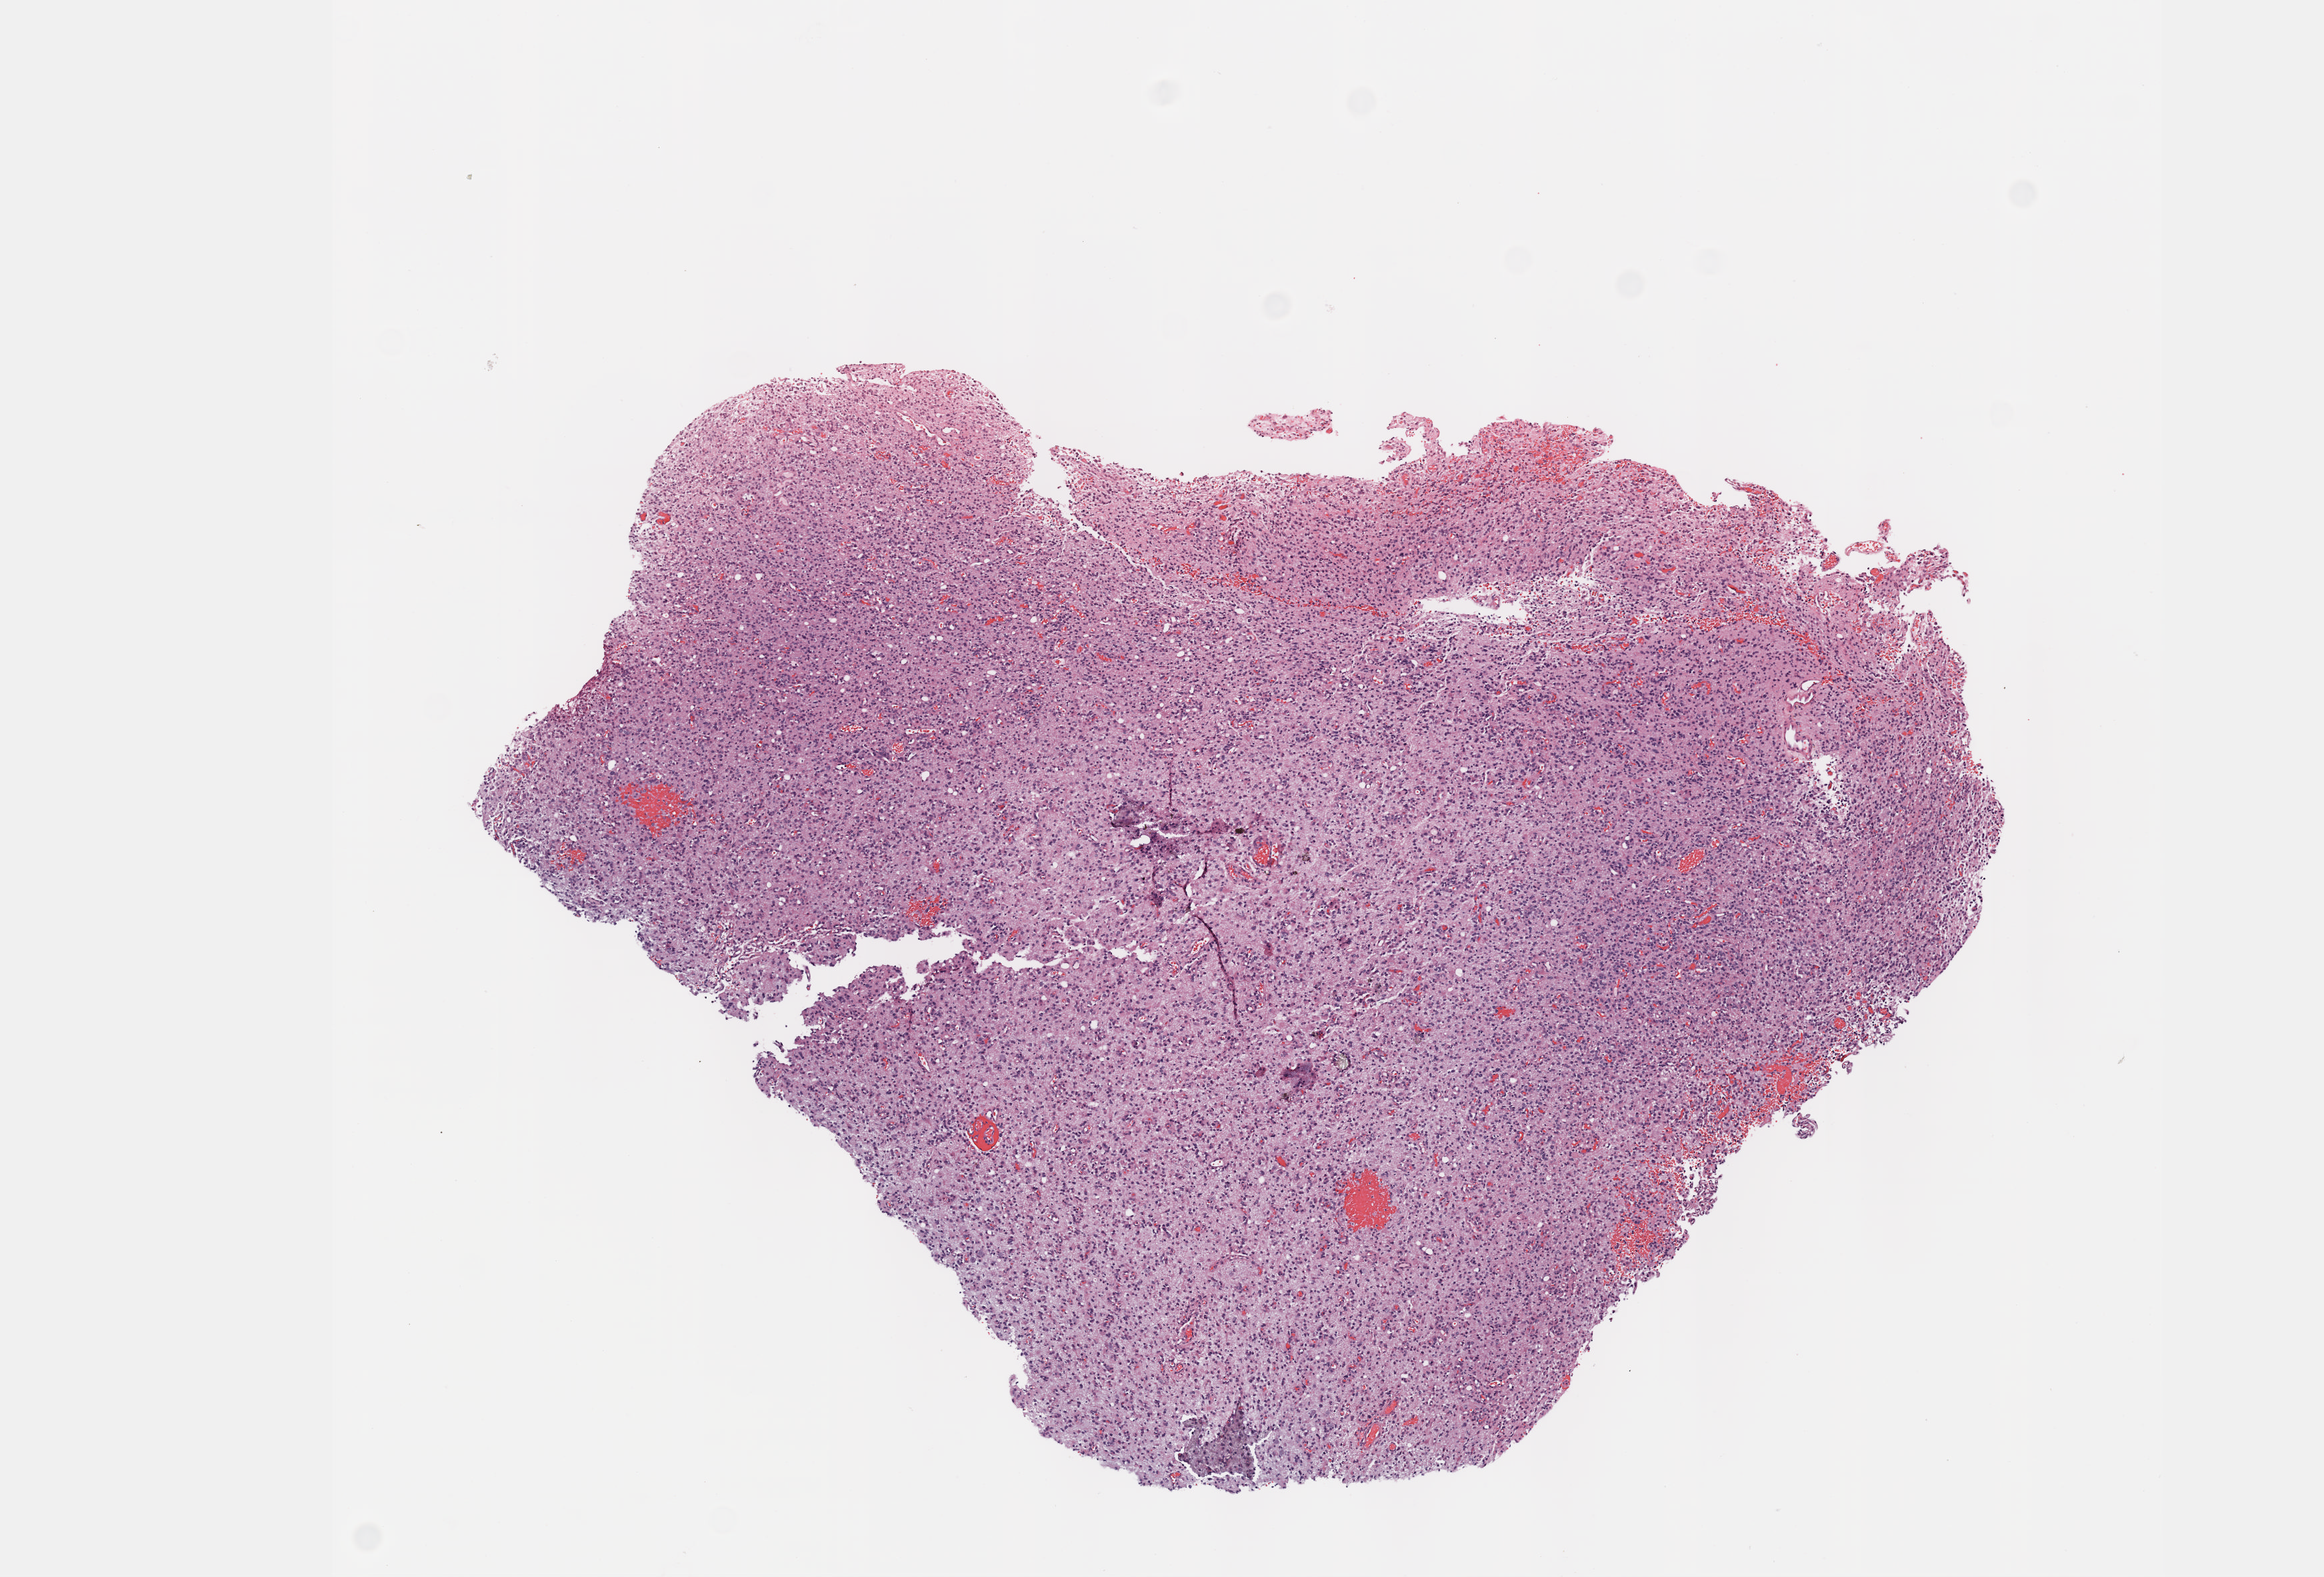
Digitized Hematoxylin and eosin (H&E) stained tissue section (whole slide) — a low-resolution overview of the entire scanned area, about 7.0 x 4.8 mm; FFPE section; primary tumour sample from the brain. Male, age 39 years at initial diagnosis.
Laterality: right. Diagnosis: Mixed glioma (cerebrum).